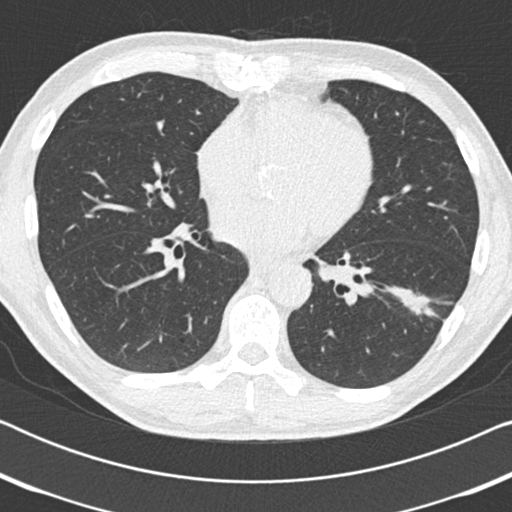
Axial slice from a low-dose chest CT screening exam. Third screening round (two years after baseline). Lung window (W 1500 / L -600 HU). Slice 105 of 186 in the series. Male participant, aged 59 years at enrolment. Current smoker at enrolment.
• Lesion marked by an expert reader, box from (x=387, y=272) to (x=455, y=334) px.
• The screening reader recorded 2 non-calcified nodules or masses ≥4 mm on this exam (left lower lobe, right middle lobe); which of them this box marks is not recorded.
• Later outcome: lung cancer diagnosed 73 days after this screen — adenocarcinoma, NOS, left lower lobe, poorly differentiated (G3), stage IA (AJCC 6th edition), 20 mm at pathology.